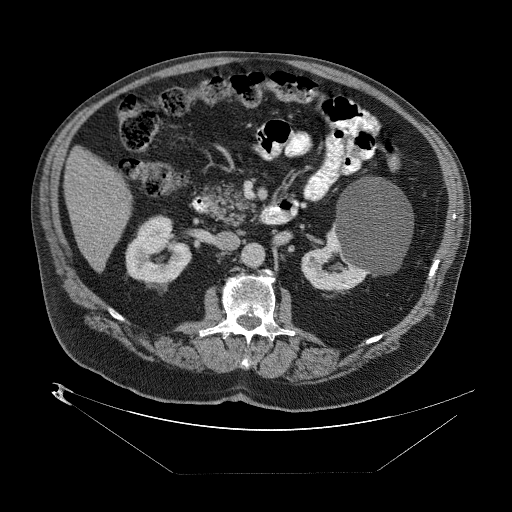
Contrast-enhanced abdominal CT (liver protocol), one axial slice; position 19 of 89 along the scan axis; reconstruction kernel STANDARD; one of 2 acquisitions stored at this slice position; soft-tissue window (W 400 / L 40 HU); 2.5 mm slice thickness; 512 × 512 image matrix, field of view 480 × 480 mm. Case-level facts recorded for this patient, not image findings: diagnosis: hepatocellular carcinoma (patient treated with transarterial chemoembolisation; whether this scan precedes or follows treatment is not stated here); TNM stage (as recorded): Stage-II; Child-Pugh class: B.
Outlined on this slice (semi-automatic segmentation, software-assisted and operator-edited):
- abdominal aorta: bounding box (x1, y1, x2, y2) in pixels: (244, 244, 265, 266)
- liver parenchyma outside the tumour (the mass and vessels are separate outlines, so this box may not span the whole liver): (62, 144, 132, 268)
- liver vessels: (88, 200, 126, 237)